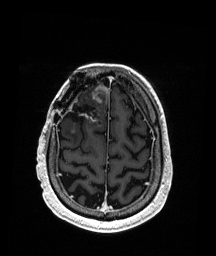
Brain MRI from a brain-tumour surgery series, one axial slice. Position 46 of 192 along the scan axis. T1-weighted post-contrast. 1 mm slice thickness. 216 × 256 image matrix, field of view 211 × 250 mm. Case-level facts recorded for this patient, not image findings: histopathology: Astrocytoma; WHO grade: 3; IDH mutation: yes.
Annotated regions visible in this slice (expert manual segmentation):
- previous resection cavity: bounding box [x1, y1, x2, y2] px = [65, 93, 101, 124]
- tumour: [93, 85, 109, 103]